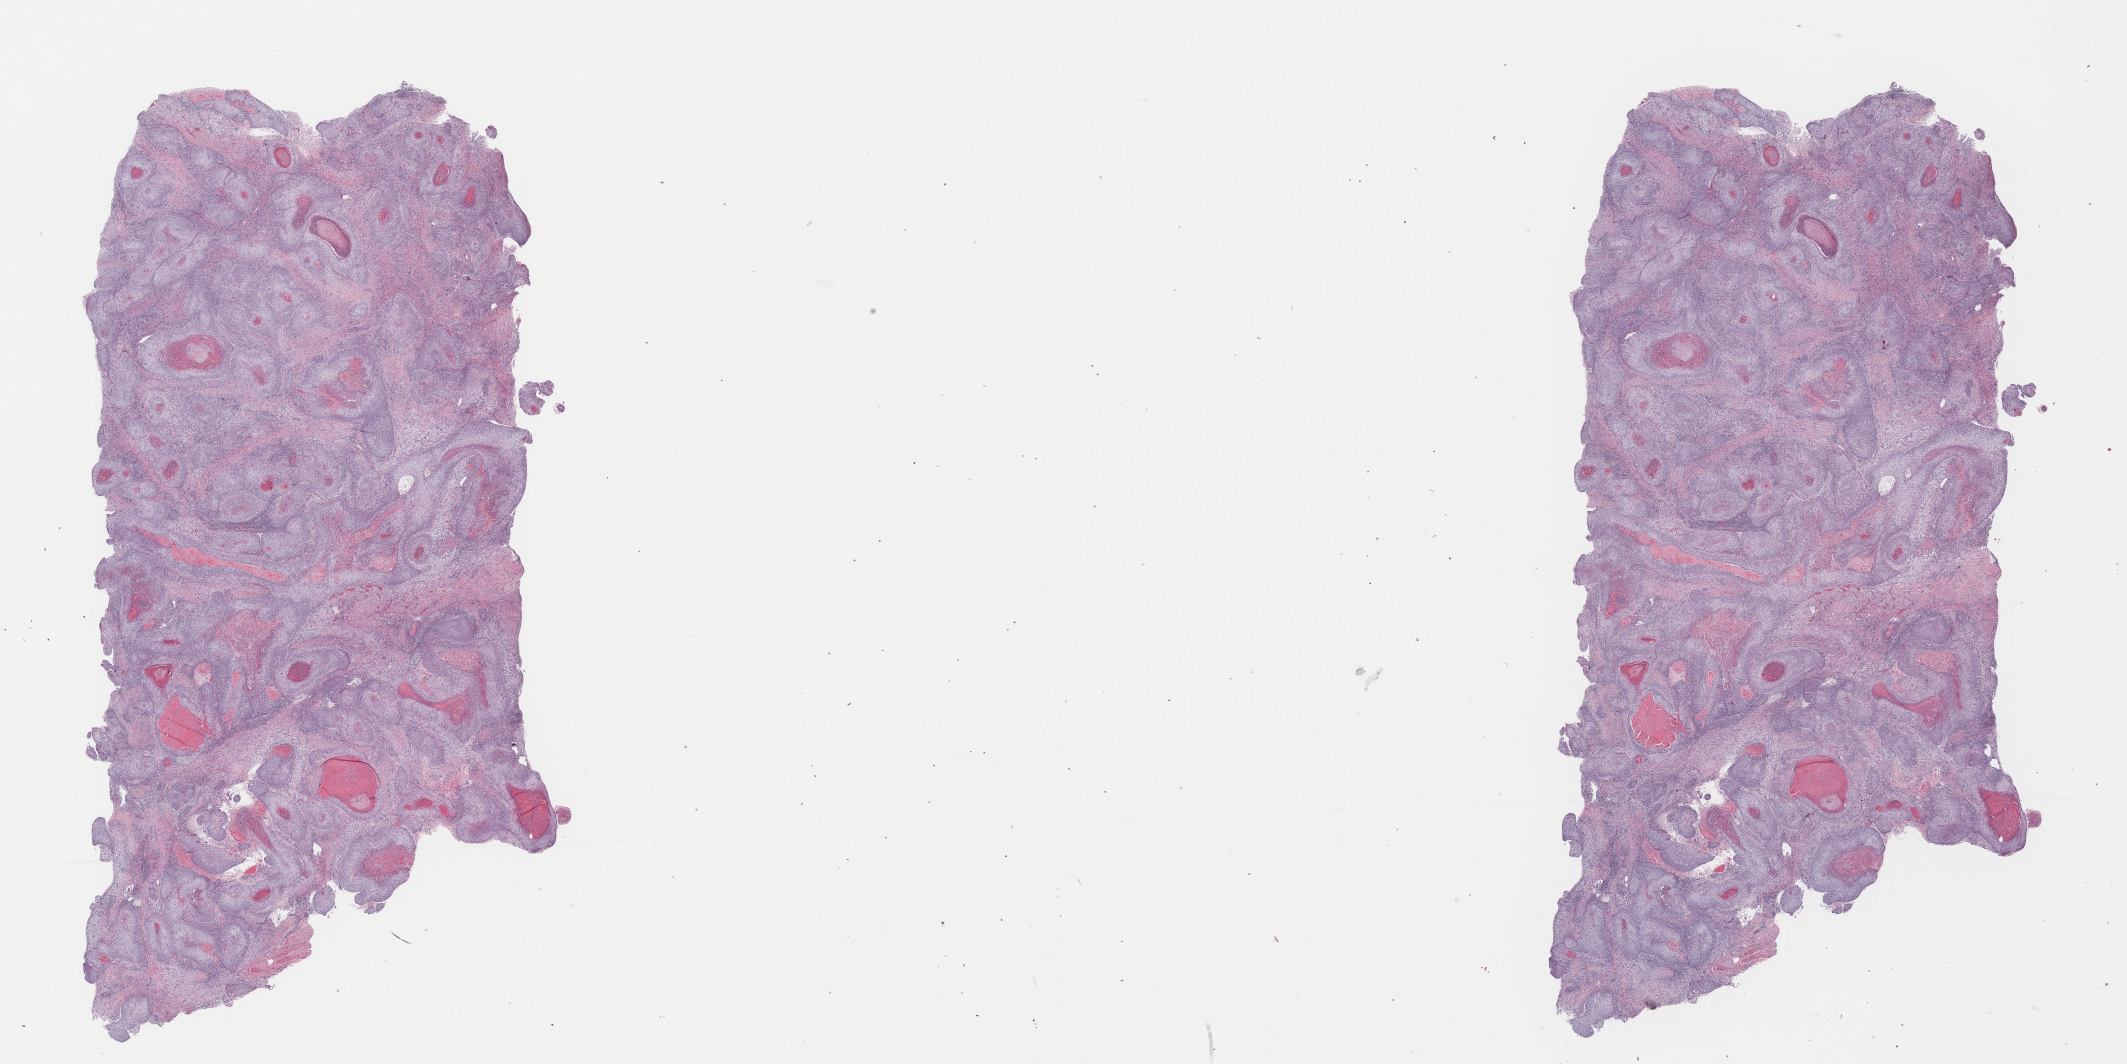
Digitized H&E tissue section (whole slide) — a low-resolution overview of the entire scanned area, about 33.6 x 16.8 mm (acquisition: 40x scan). Formalin-fixed paraffin-embedded (FFPE) diagnostic section. Primary tumour sample from the head and neck. Male, age 59 years at initial diagnosis. Histologic grade: G2 (moderately differentiated).
Pathologic diagnosis: Squamous cell carcinoma, NOS (cheek mucosa). AJCC pathologic stage: IVA. TNM: T4a N0 MX. Lymph nodes positive (case pathology): 0 of 45 examined.